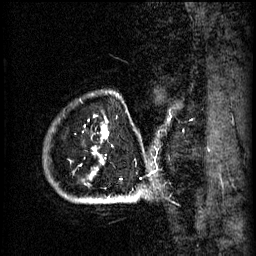
Breast MRI (dynamic contrast-enhanced), one sagittal slice. Position 56 of 60 along the scan axis. 3 images stored at this slice position (order not interpretable as contrast timing). 1.5 T. TE 4.2 ms, TR 11 ms. 2 mm slice thickness. 256 × 256 image matrix, field of view 200 × 200 mm. Patient: female, 51 years.
Annotated regions visible in this slice (semi-automatically segmented with operator editing):
- analysis volume of interest (the breast-tissue region the enhancement analysis was run in; not a lesion): bounding box <57,94,159,197> (left, top, right, bottom; pixels)
- tumour enhancement mask (voxels above the 70 % enhancement threshold inside the analysis volume of interest): <103,126,123,181>